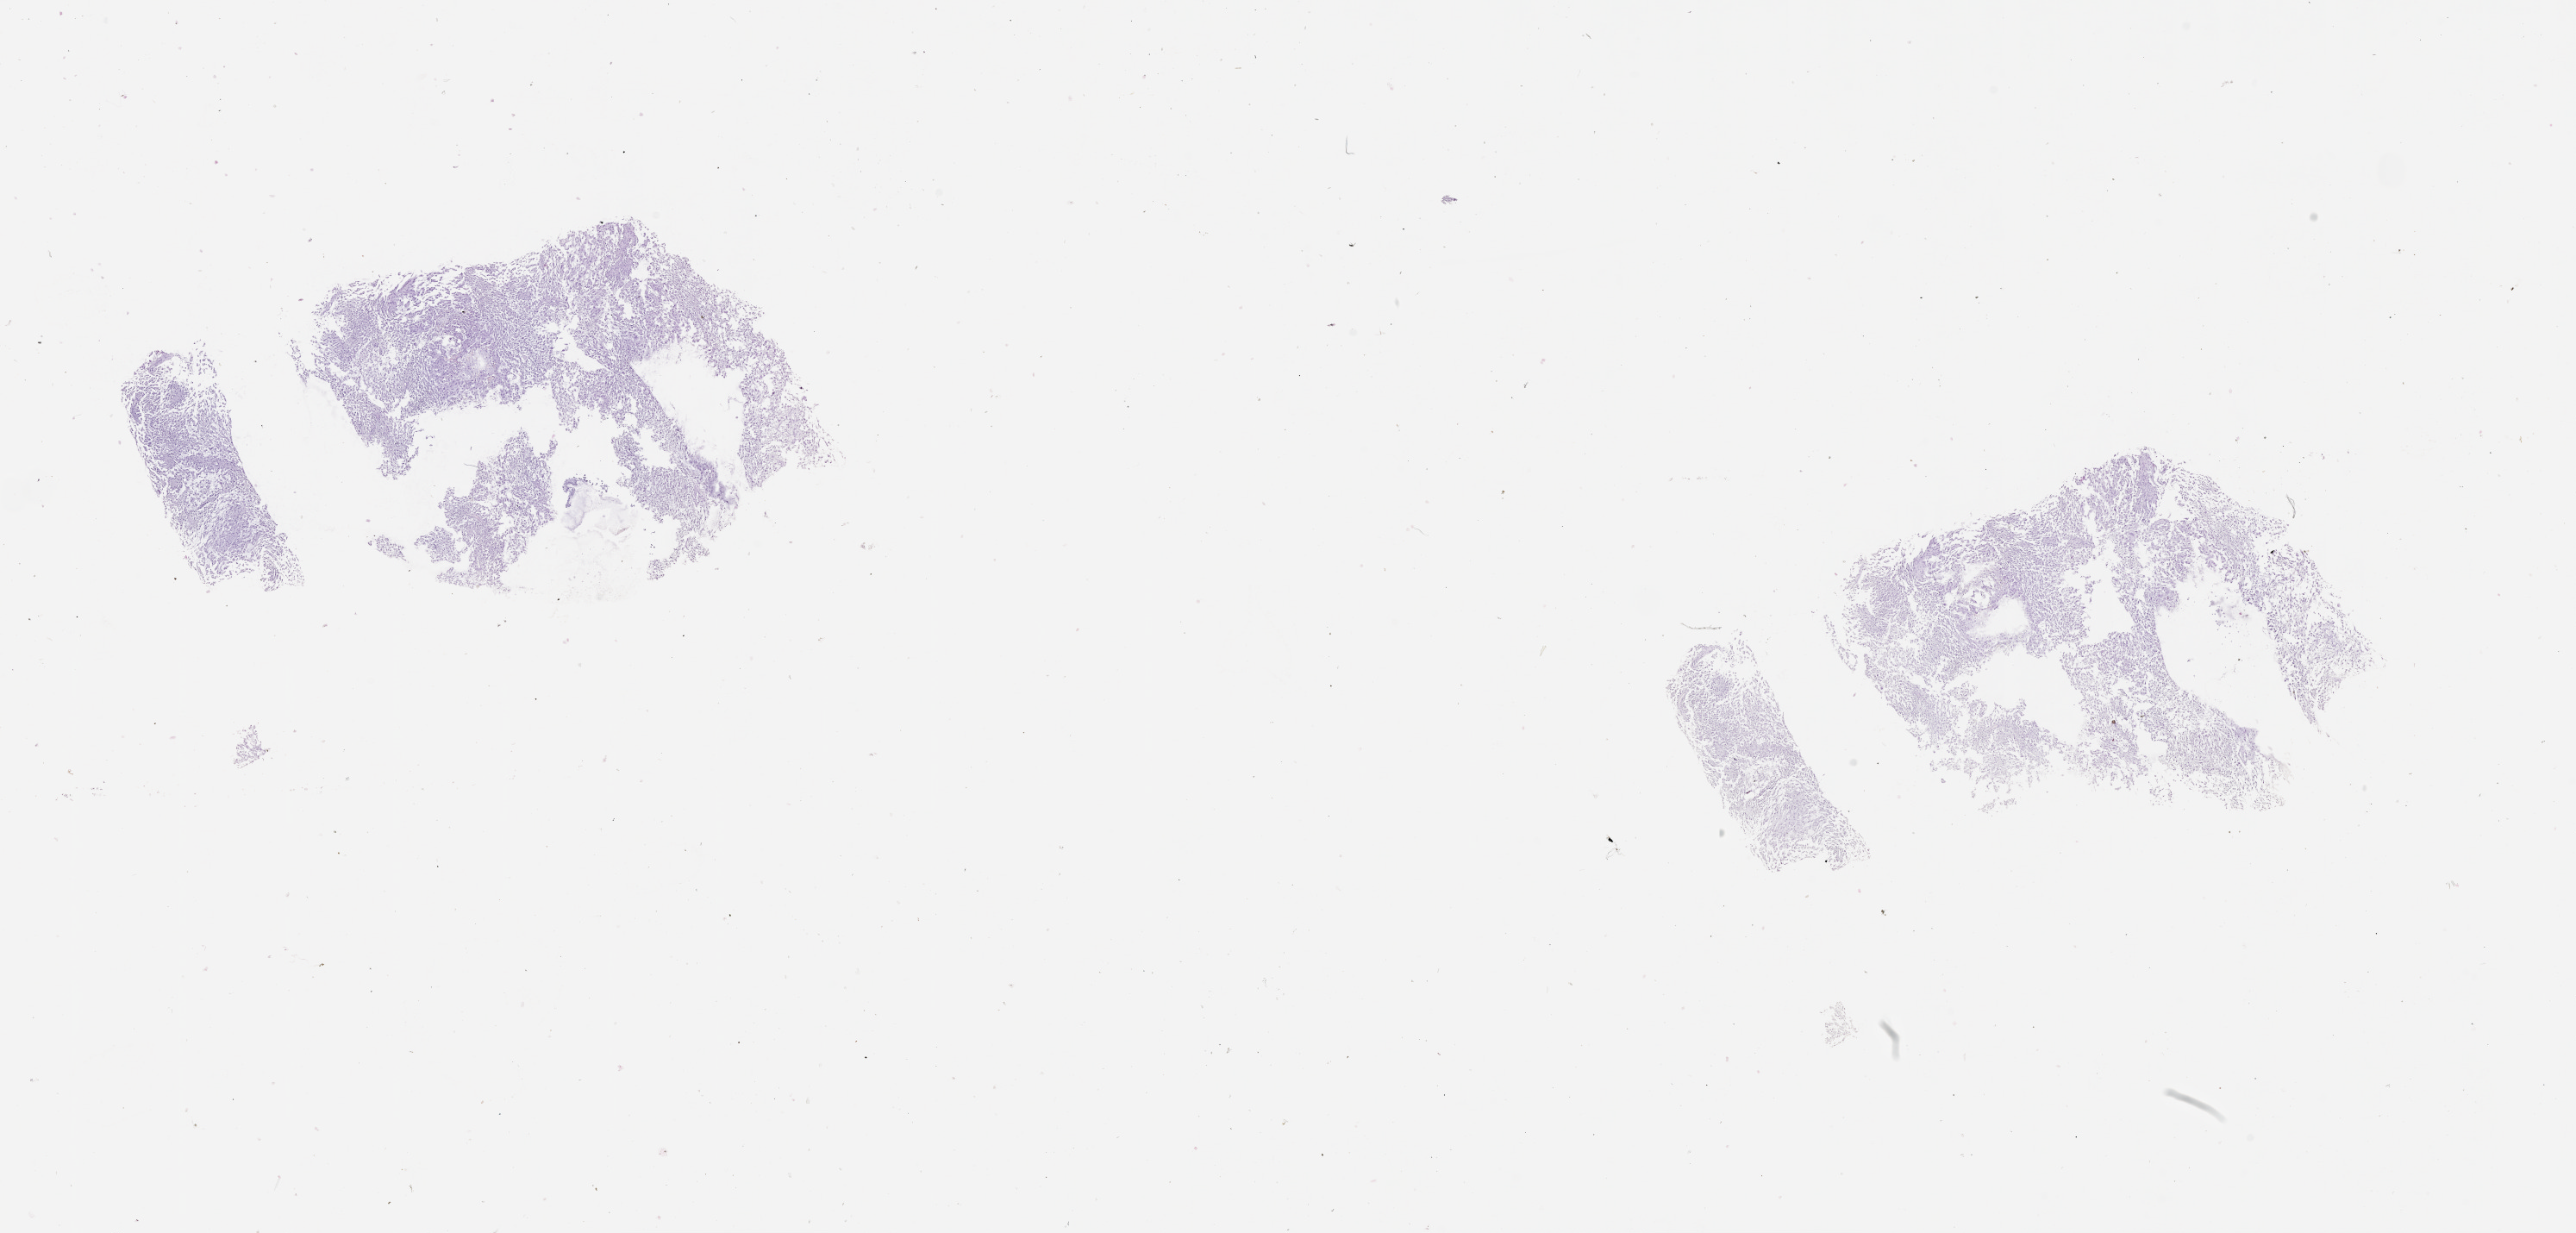
Digitized Hematoxylin and eosin (H&E) stained tissue section (whole slide), a low-resolution overview of the entire scanned area, about 24.1 x 11.5 mm, tumour tissue sample, sampled site: brain. Patient: male, age 65 years. Slide review estimates, as recorded: tumour nuclei 70%, necrosis 15%.
- primary tumour site (as recorded): parietal lobe
- diagnosis: Glioblastoma